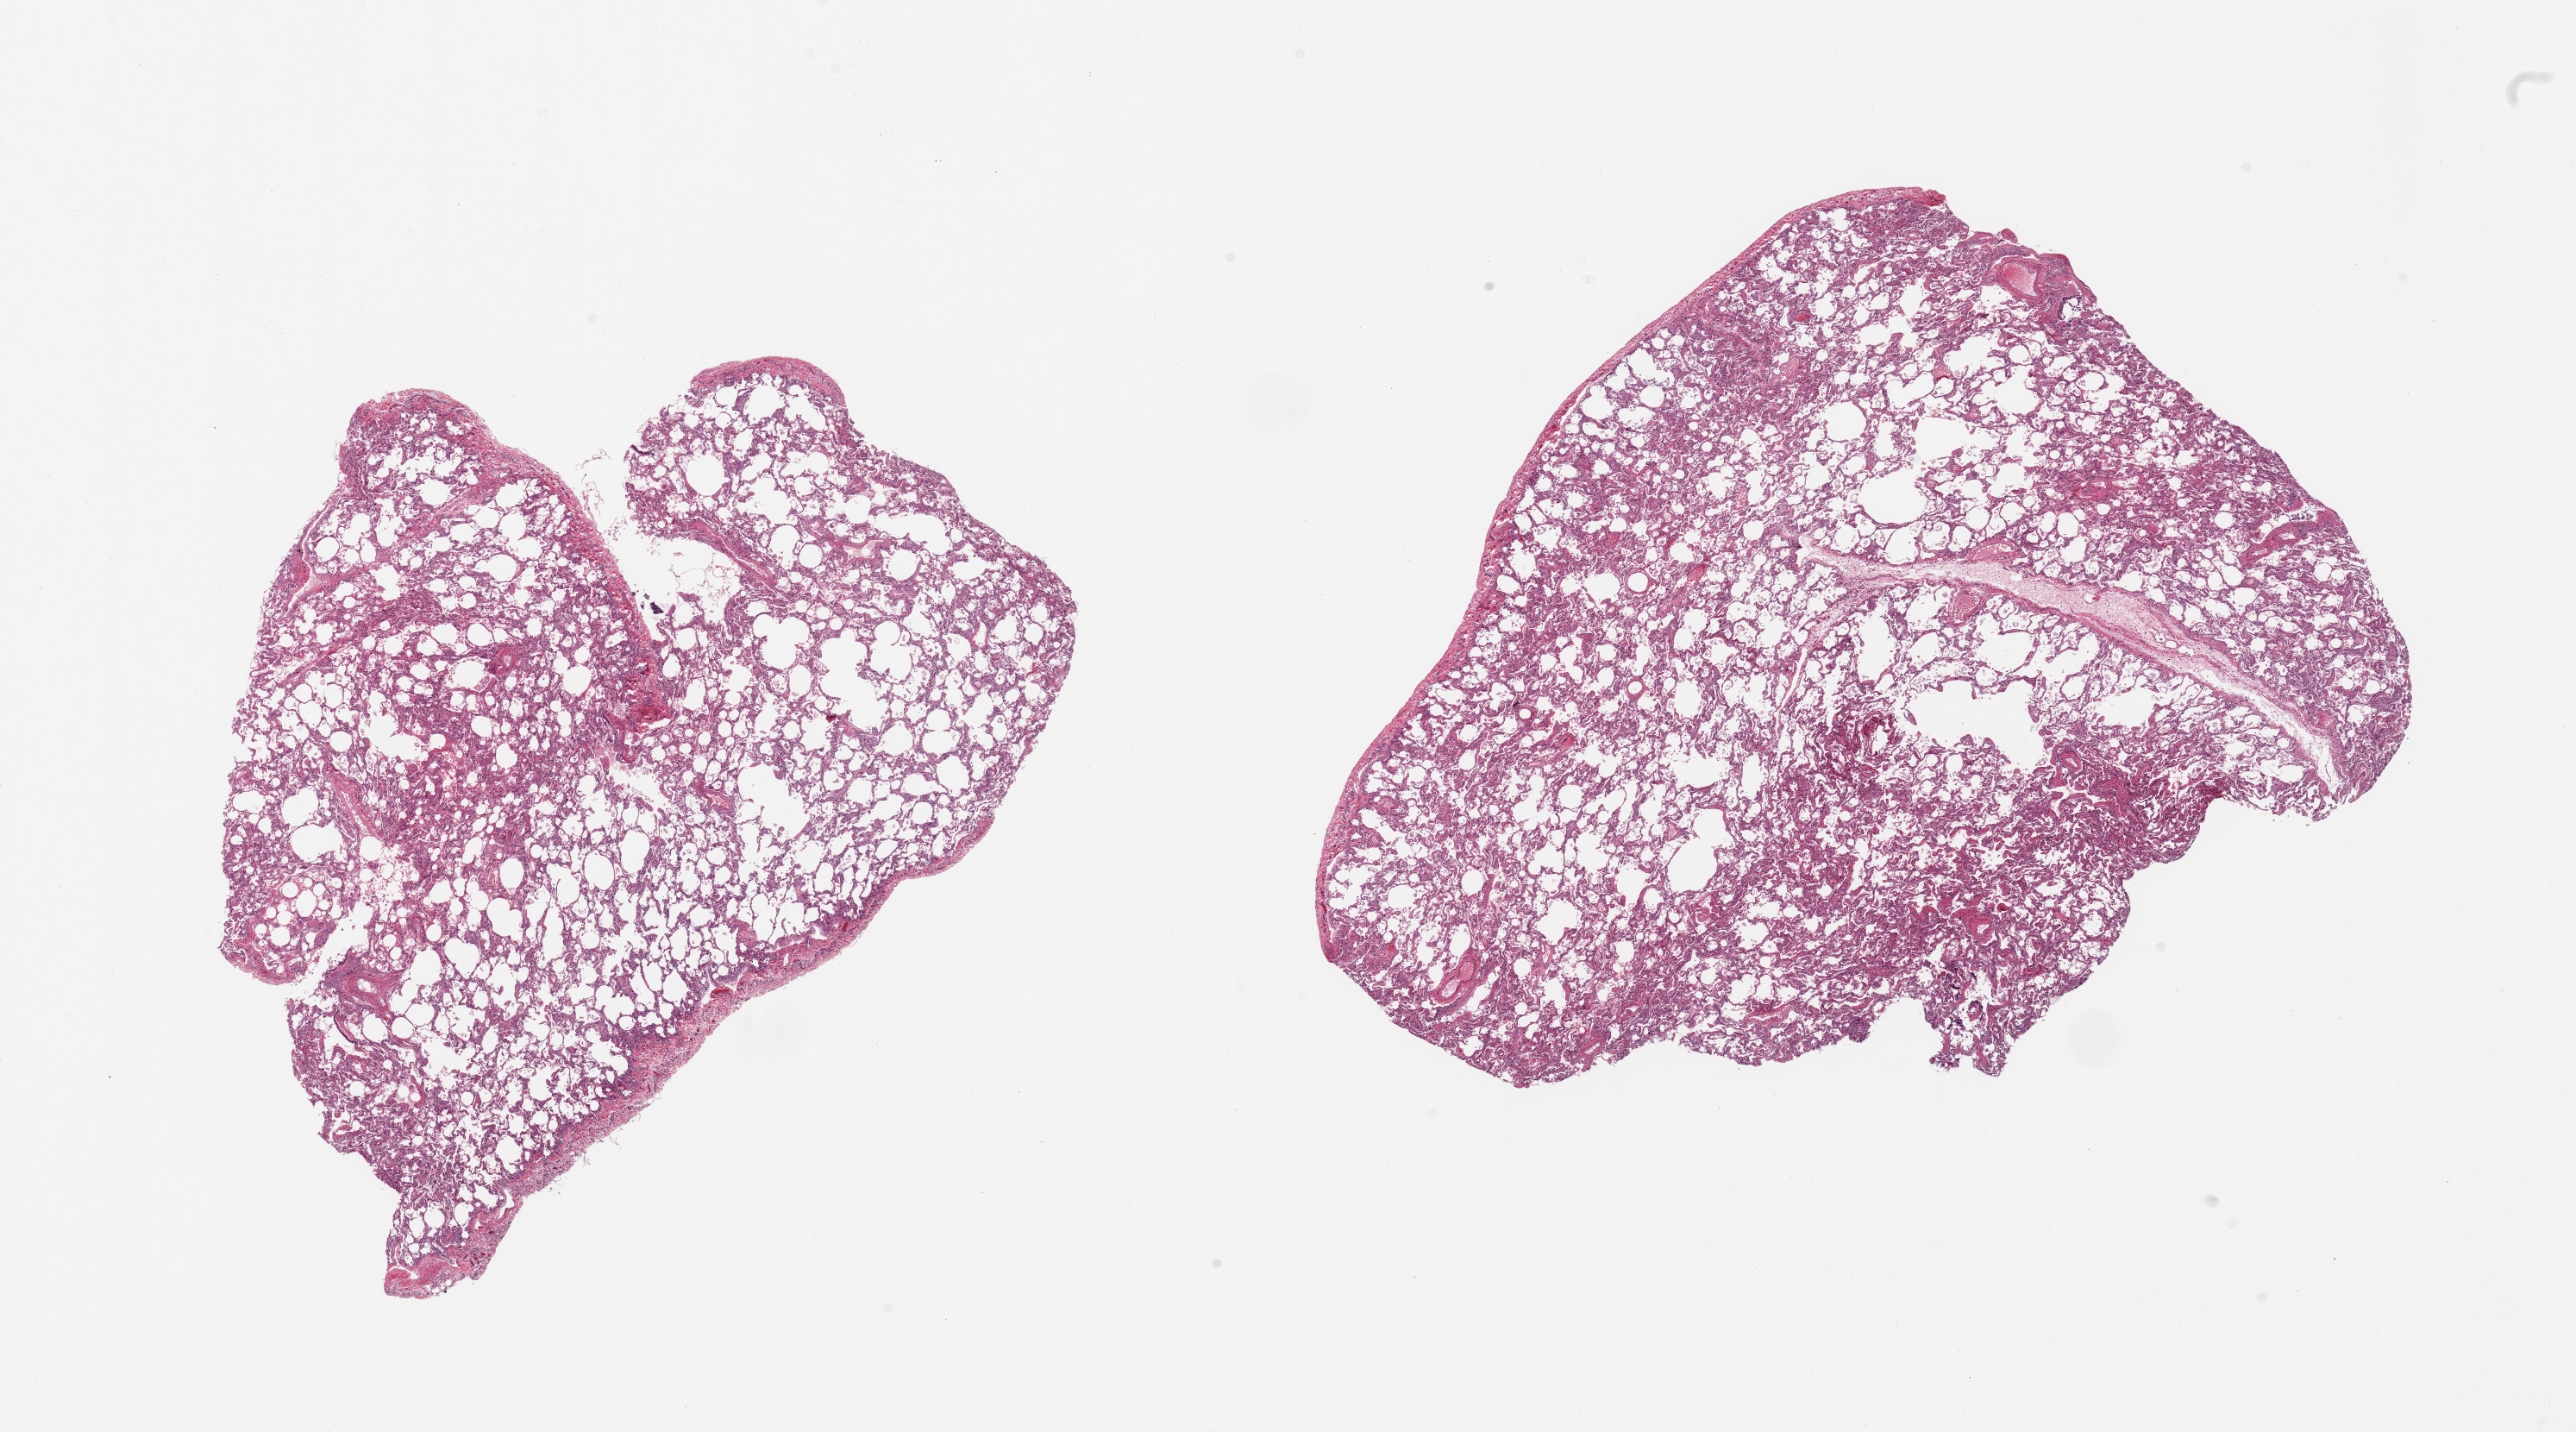
Hematoxylin and eosin (H&E) whole-slide image, brightfield, low-resolution overview of the scanned area, about 23.6 x 13.1 mm (acquisition: 20x scan). PAXgene-fixed paraffin-embedded (PFPE) section. Sampled site (target tissue): lung. Tissue donor sample. Donor: female.
Review note (as recorded): 2 pieces; congestion, includes pleura (target is 1 cm below pleura).